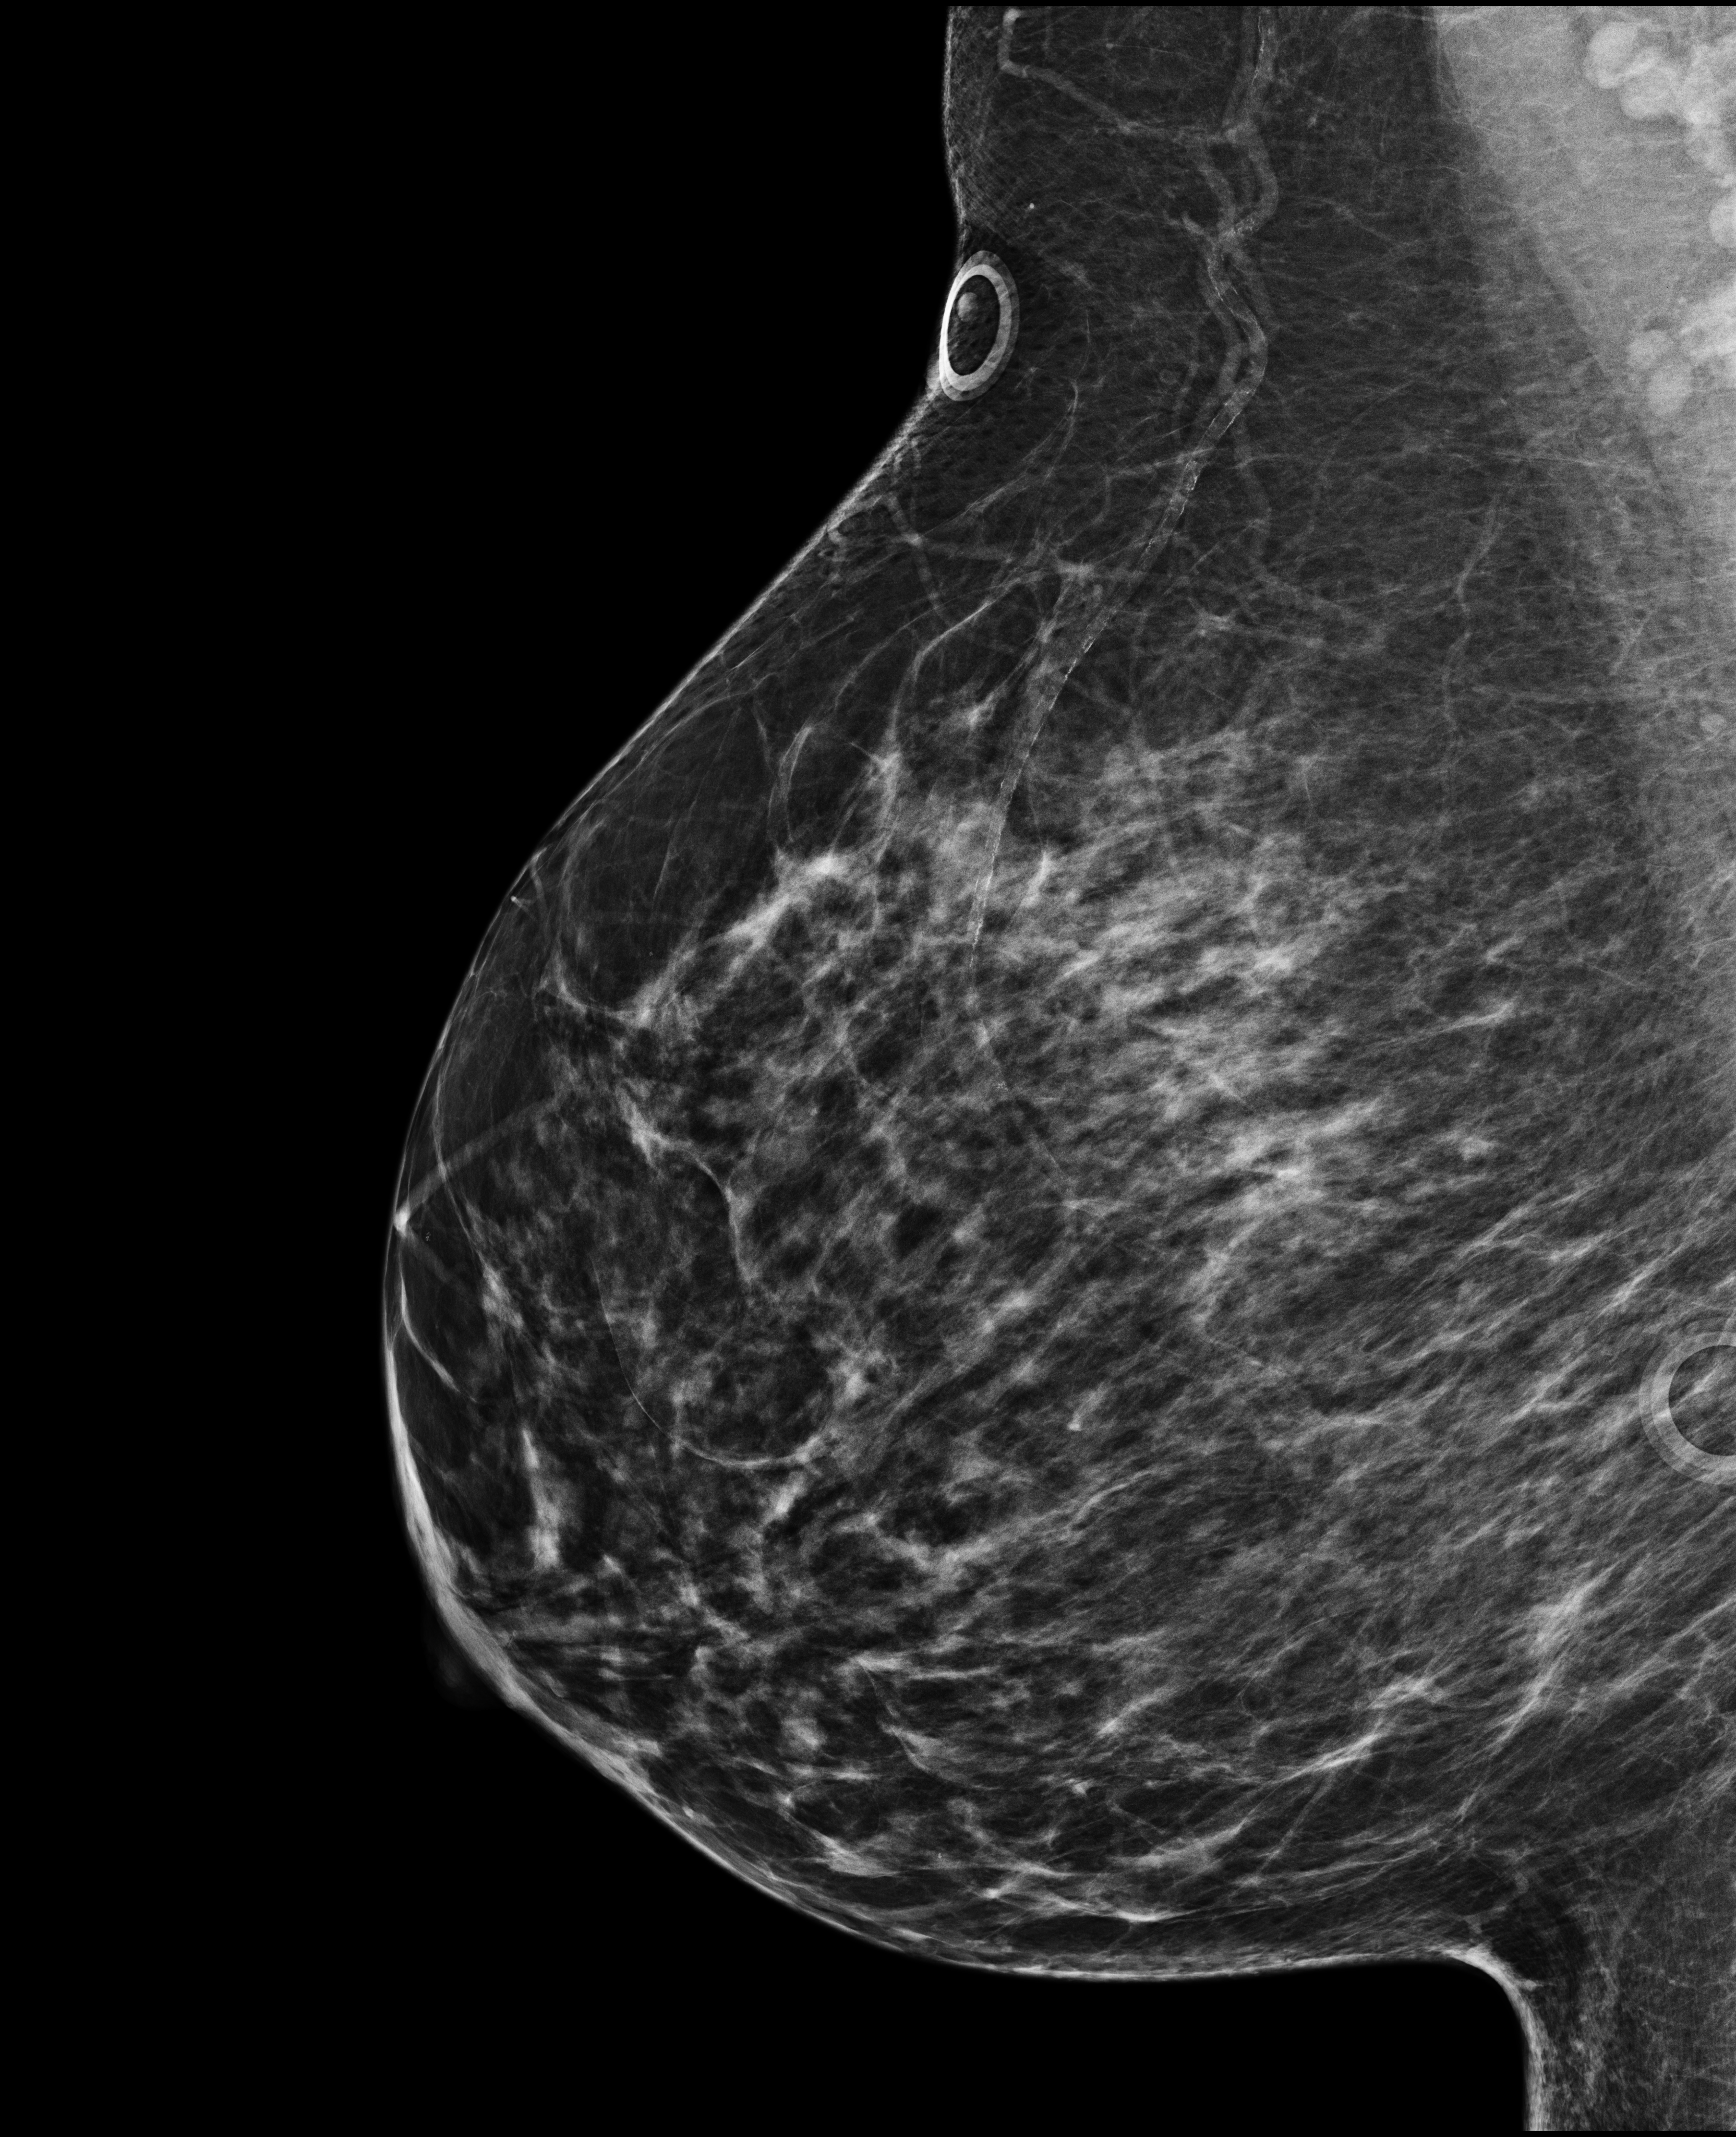
Digital mammogram (FFDM); right breast; medio-lateral oblique projection; annual screening mammography examination. Female patient, age 67 years.
BI-RADS breast density category at the screening exam (both breasts, scale 1–4): 2. Final BI-RADS category for the screening round (tomosynthesis exam, both breasts): category 1. Recall: no recall after this screen.